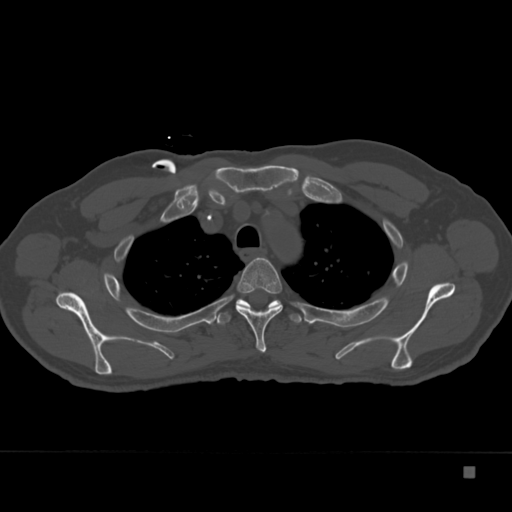
CT including the spine, one axial slice; slice 282 of 332 in the series (ordered by position); bone window (W 1800 / L 400 HU); 1.5 mm slice thickness; 512 × 512 image matrix, field of view 389 × 389 mm. Patient: male, 72 years. Case-level facts recorded for this patient, not image findings: primary cancer: skeletal.
Annotated regions visible in this slice (semi-automatic segmentation, software-assisted and operator-edited):
- T3 vertebra: bounding box <236,257,283,353> (left, top, right, bottom; pixels)
- T4 vertebra: <214,298,302,325>